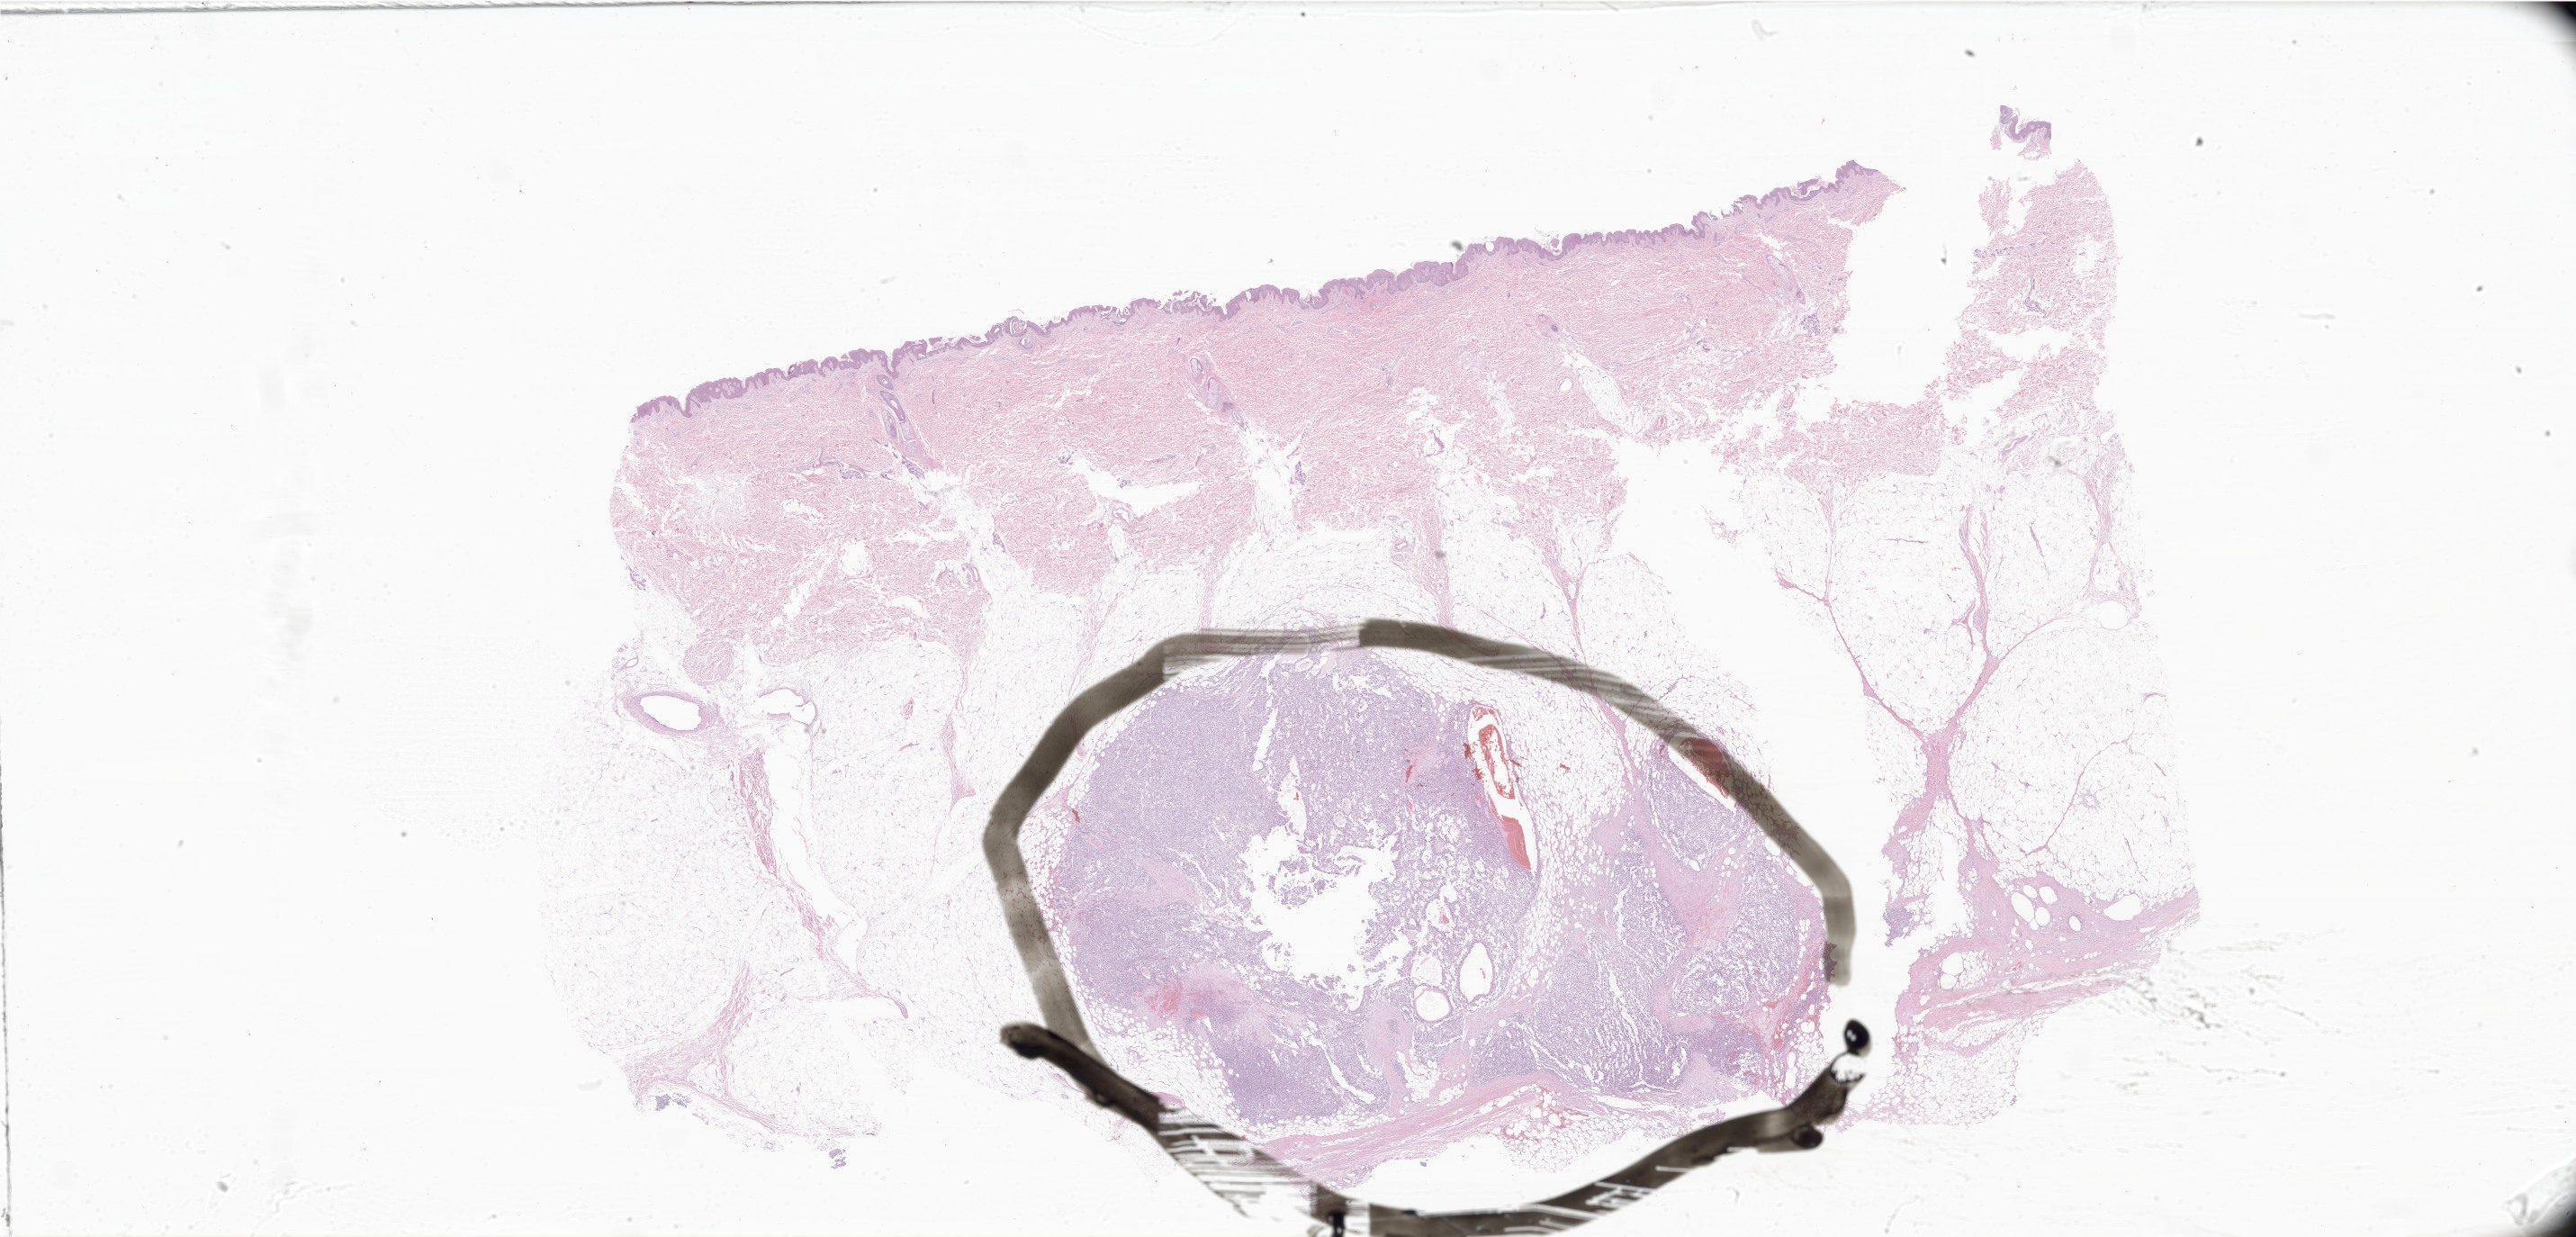
Whole-slide image, haematoxylin and eosin stain of tumor tissue from the soft tissue, shown as a low-resolution overview of the whole scanned area (about 48.3 x 23.2 mm); FFPE section. Female patient, age 126 months (10 years 6 months).
Recorded diagnosis: Sarcoma, NOS.